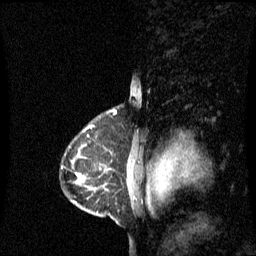
Breast MRI (dynamic contrast-enhanced), one sagittal slice; slice 42 of 60 in the series (ordered by position); dynamic contrast-enhanced series, image 2 of 3 at this slice position (ordered by acquisition); 1.5 T; TE 4.2 ms, TR 8.4 ms; 256 × 256 image matrix, field of view 240 × 240 mm. Patient: female, 42 years. Case-level facts recorded for this patient, not image findings: setting: breast cancer imaged before/during neoadjuvant chemotherapy; receptor status: HR-positive, HER2-negative.
Structures marked on this image (semi-automatic segmentation, software-assisted and operator-edited):
- analysis volume of interest (the breast-tissue region the enhancement analysis was run in; not a lesion): box from (x=78, y=118) to (x=135, y=195) px
- tumour enhancement mask (voxels above the 70 % enhancement threshold inside the analysis volume of interest): (x=132, y=166)–(x=133, y=171)